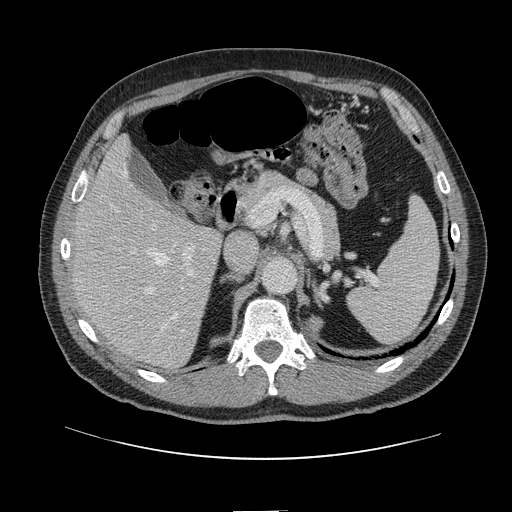
Contrast-enhanced abdominal CT, one axial slice; position 79 of 161 along the scan axis; 120 kVp; soft-tissue window (W 400 / L 40 HU); 2.5 mm slice thickness; 512 × 512 image matrix, field of view 412 × 412 mm. Male patient, age 66 years. From the clinical record (not read from this slice): diagnosis: colorectal cancer liver metastases, imaged before liver resection; multiple liver metastases: no.
Structures marked on this image (expert manual segmentation):
- hepatic veins: box from (x=122, y=171) to (x=177, y=331) px
- liver: (x=75, y=139)–(x=221, y=368)
- planned liver remnant (the part of the liver to remain after resection): (x=75, y=140)–(x=201, y=298)
- portal vein (with intrahepatic branches): (x=122, y=222)–(x=196, y=278)